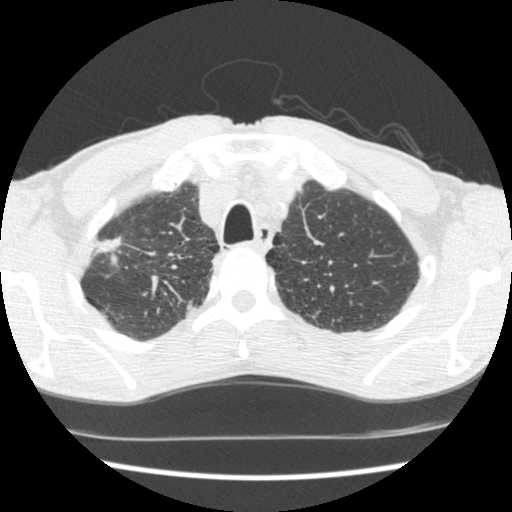
Axial slice from a low-dose chest CT screening exam. First (baseline) screen. Lung window (W 1500 / L -600 HU). Standard (soft-tissue) reconstruction kernel (STANDARD). 120 kVp. Male, age 62 years at enrolment. Current smoker at enrolment.
- Expert-annotated lung lesion, bounding box (x1, y1, x2, y2) in pixels: (81, 220, 134, 273).
- No non-calcified nodule or mass ≥4 mm was recorded by the screening reader at this exam.
- Official screen result: negative screen, significant abnormalities not suspicious for lung cancer.